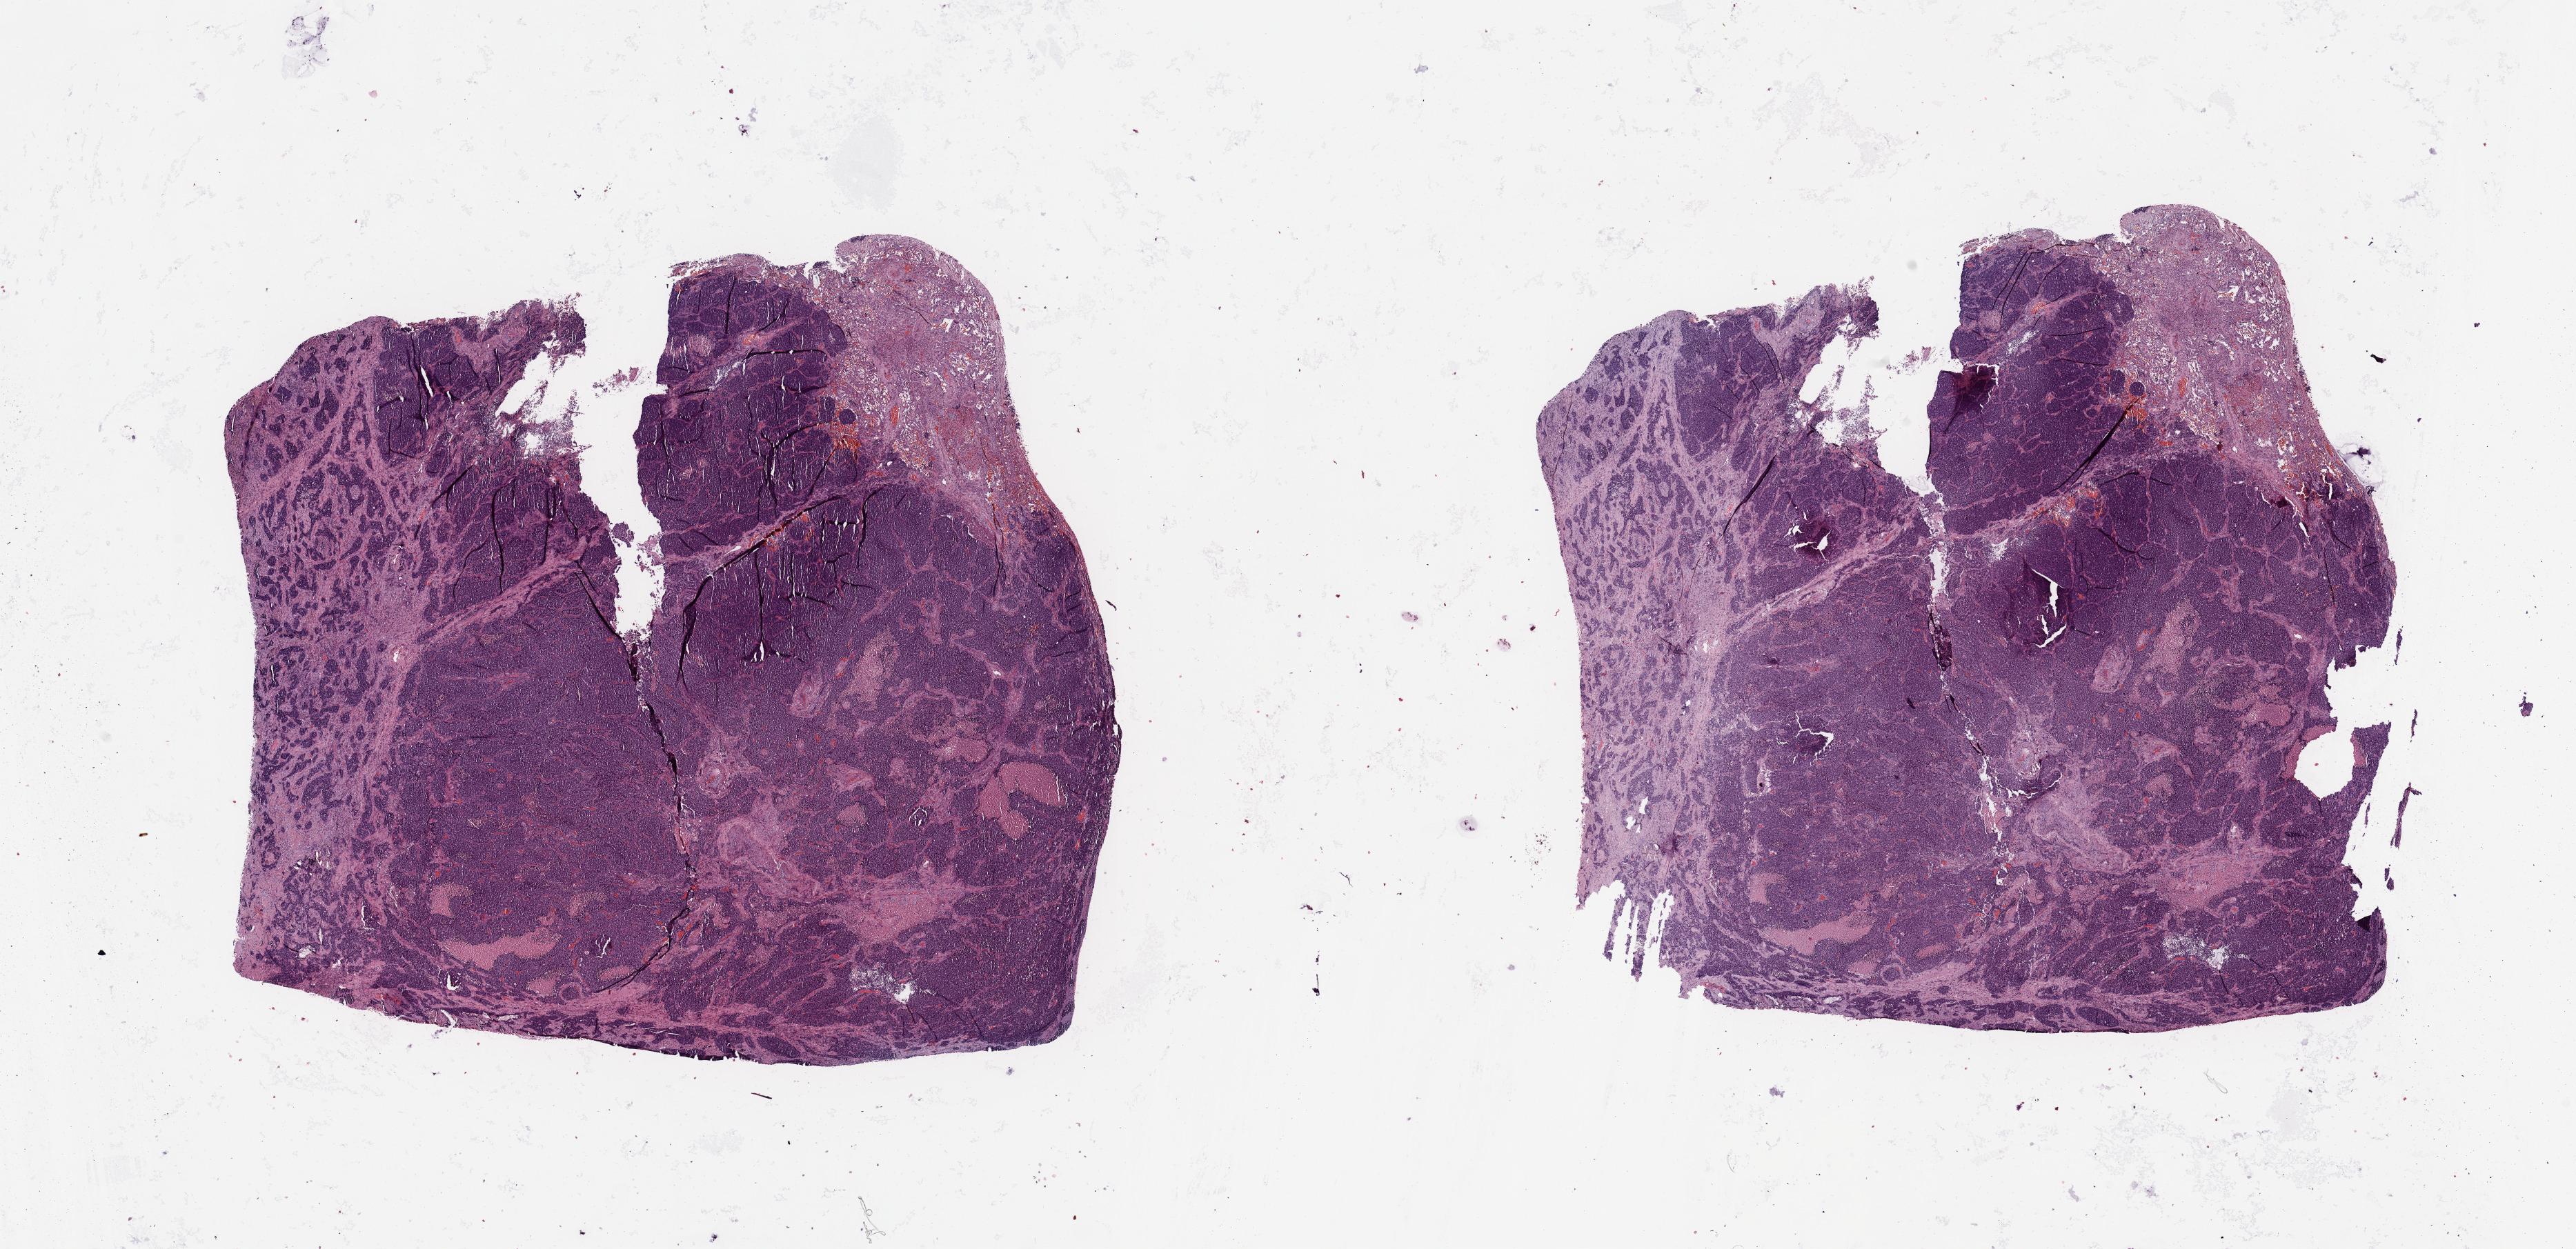
Whole-slide histology image, Hematoxylin and eosin (H&E) stained — shown as a low-resolution overview of the whole scanned area (about 29.5 x 14.3 mm), lung, tumour tissue. Patient: male, age 63 years.
Primary tumour site (as recorded): left upper lobe. Patient diagnosis (cohort enrolment): squamous cell carcinoma (lung).